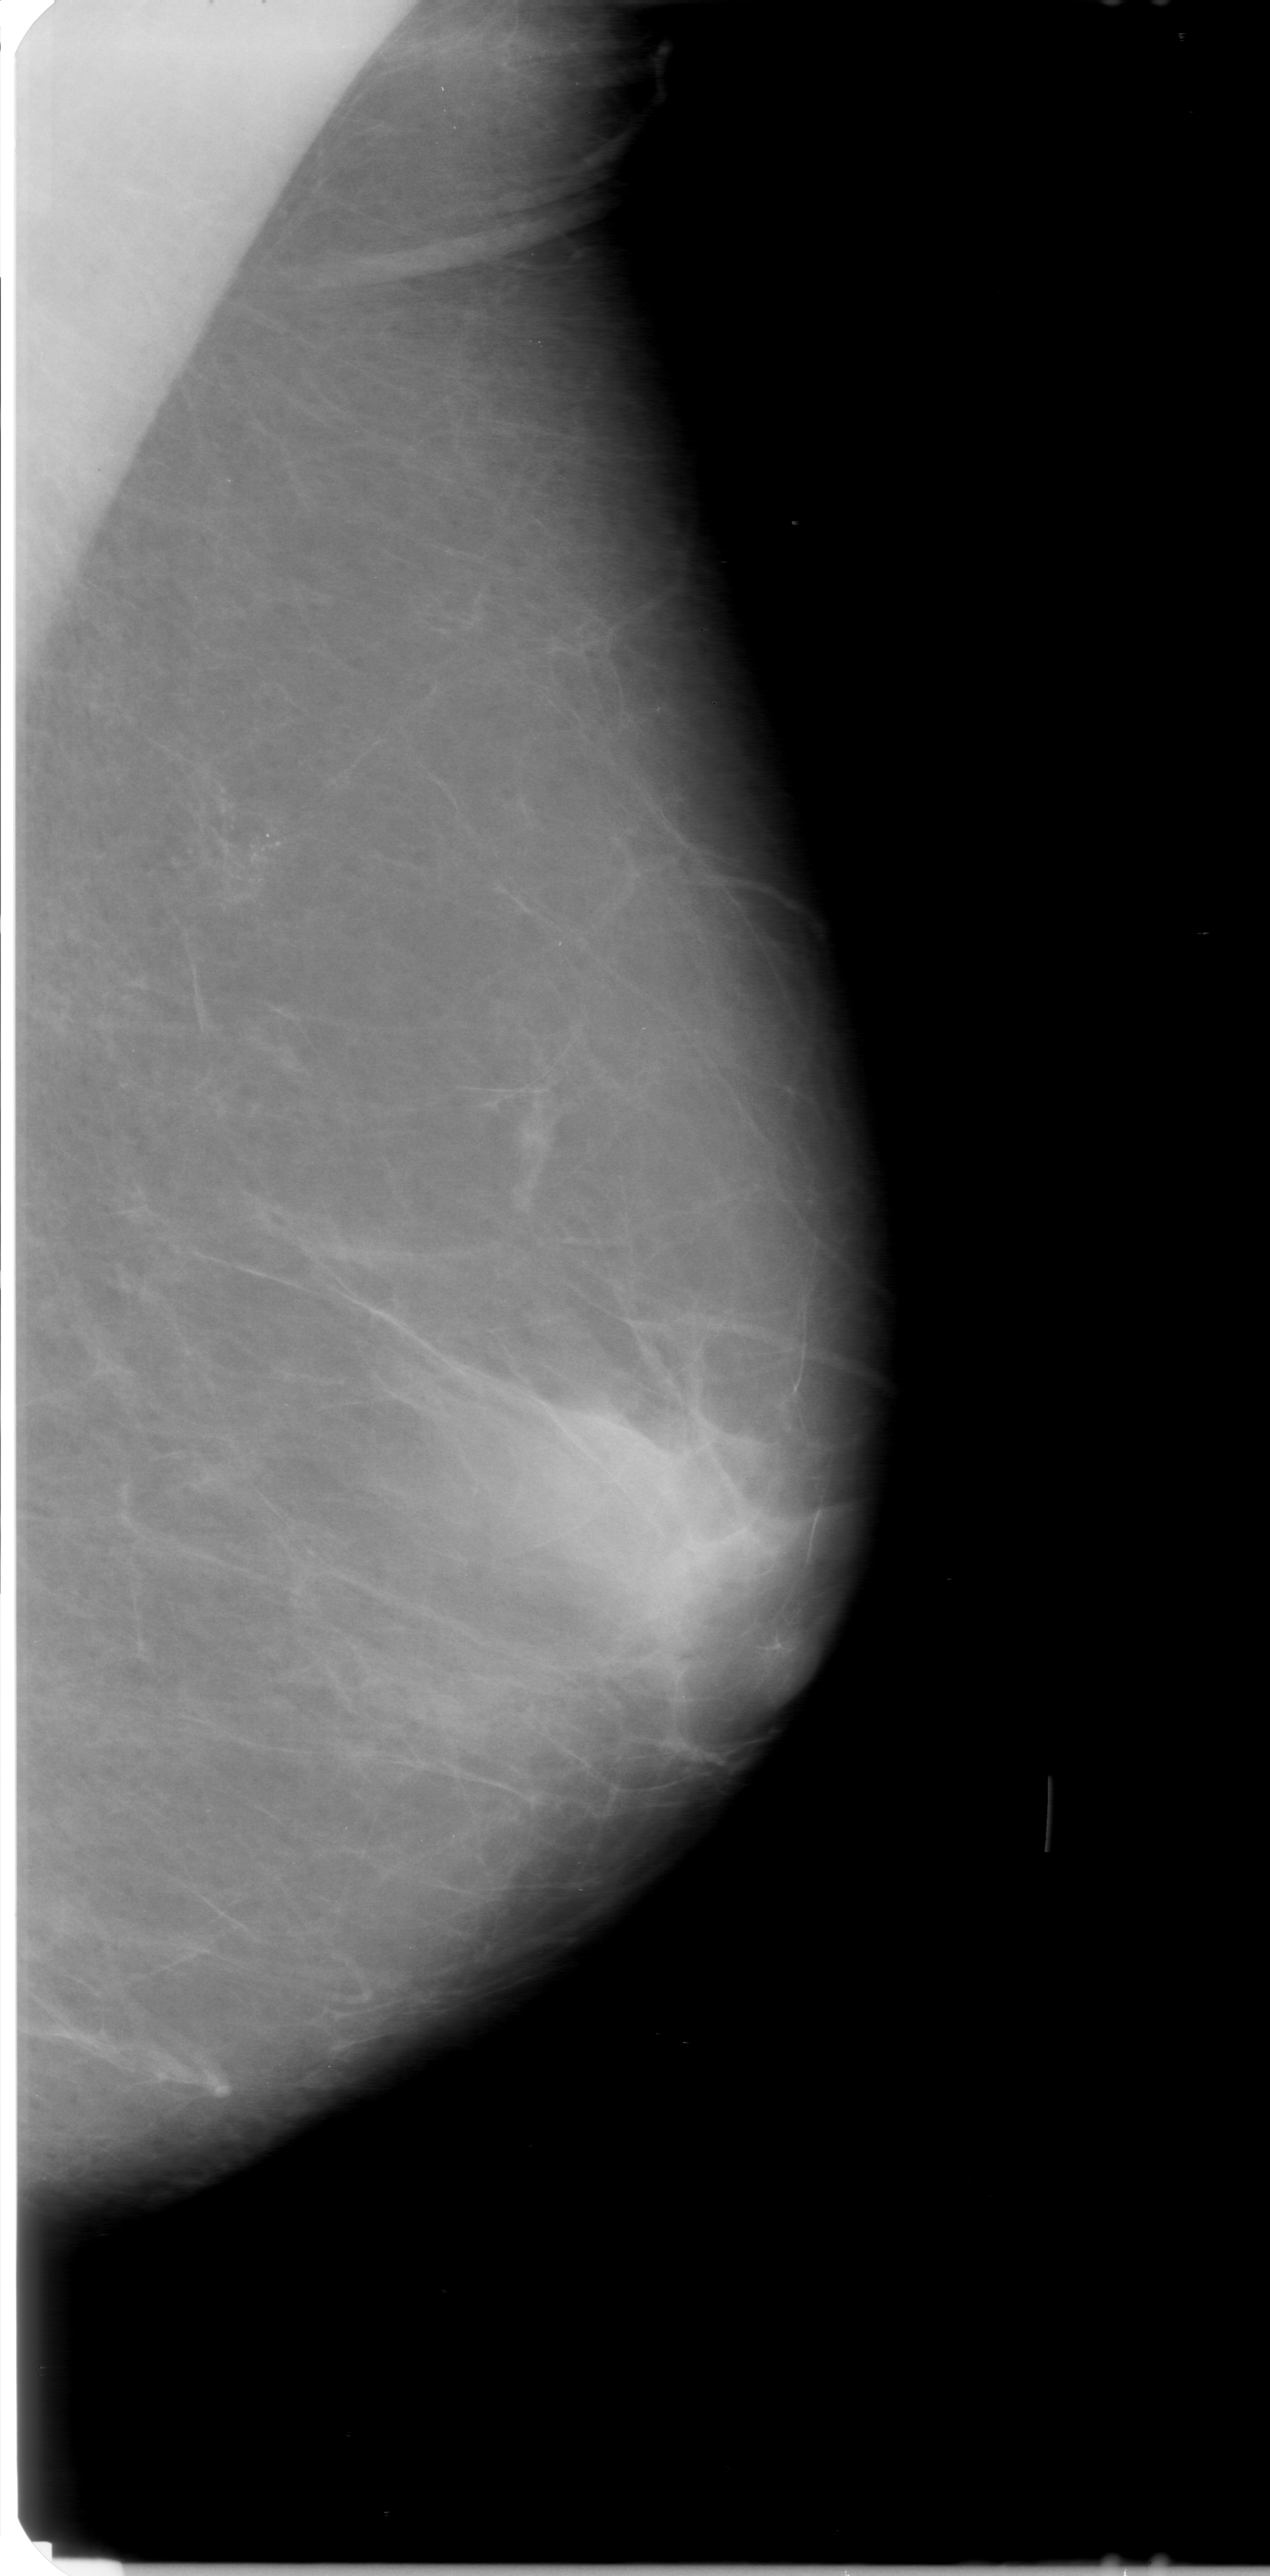
Digitized screen-film mammogram; left breast; MLO view; breast composition: almost entirely fatty (BI-RADS density category 1 of 4).
Abnormality record for this image: calcifications, morphology fine linear branching, distribution clustered; BI-RADS assessment category 0 (incomplete: needs additional imaging); subtlety rating 4 on a 1 (subtle) to 5 (obvious) scale; pathology result (as recorded, not read from the image): malignant.